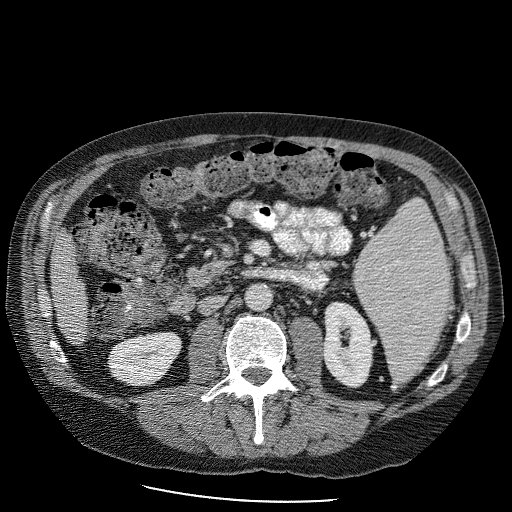
Contrast-enhanced abdominal CT (liver protocol), one axial slice. Reconstruction kernel STANDARD. Soft-tissue window (W 400 / L 40 HU). 2.5 mm slice thickness. 512 × 512 image matrix, field of view 400 × 400 mm. From the clinical record (not read from this slice): diagnosis: hepatocellular carcinoma (patient treated with transarterial chemoembolisation; whether this scan precedes or follows treatment is not stated here); TNM stage (as recorded): Stage-II; Child-Pugh class: B; tumour nodularity: uninodular.
Outlined on this slice (semi-automatic segmentation, software-assisted and operator-edited):
- liver parenchyma outside the tumour (the mass and vessels are separate outlines, so this box may not span the whole liver): bounding box (x1, y1, x2, y2) in pixels: (50, 221, 92, 344)